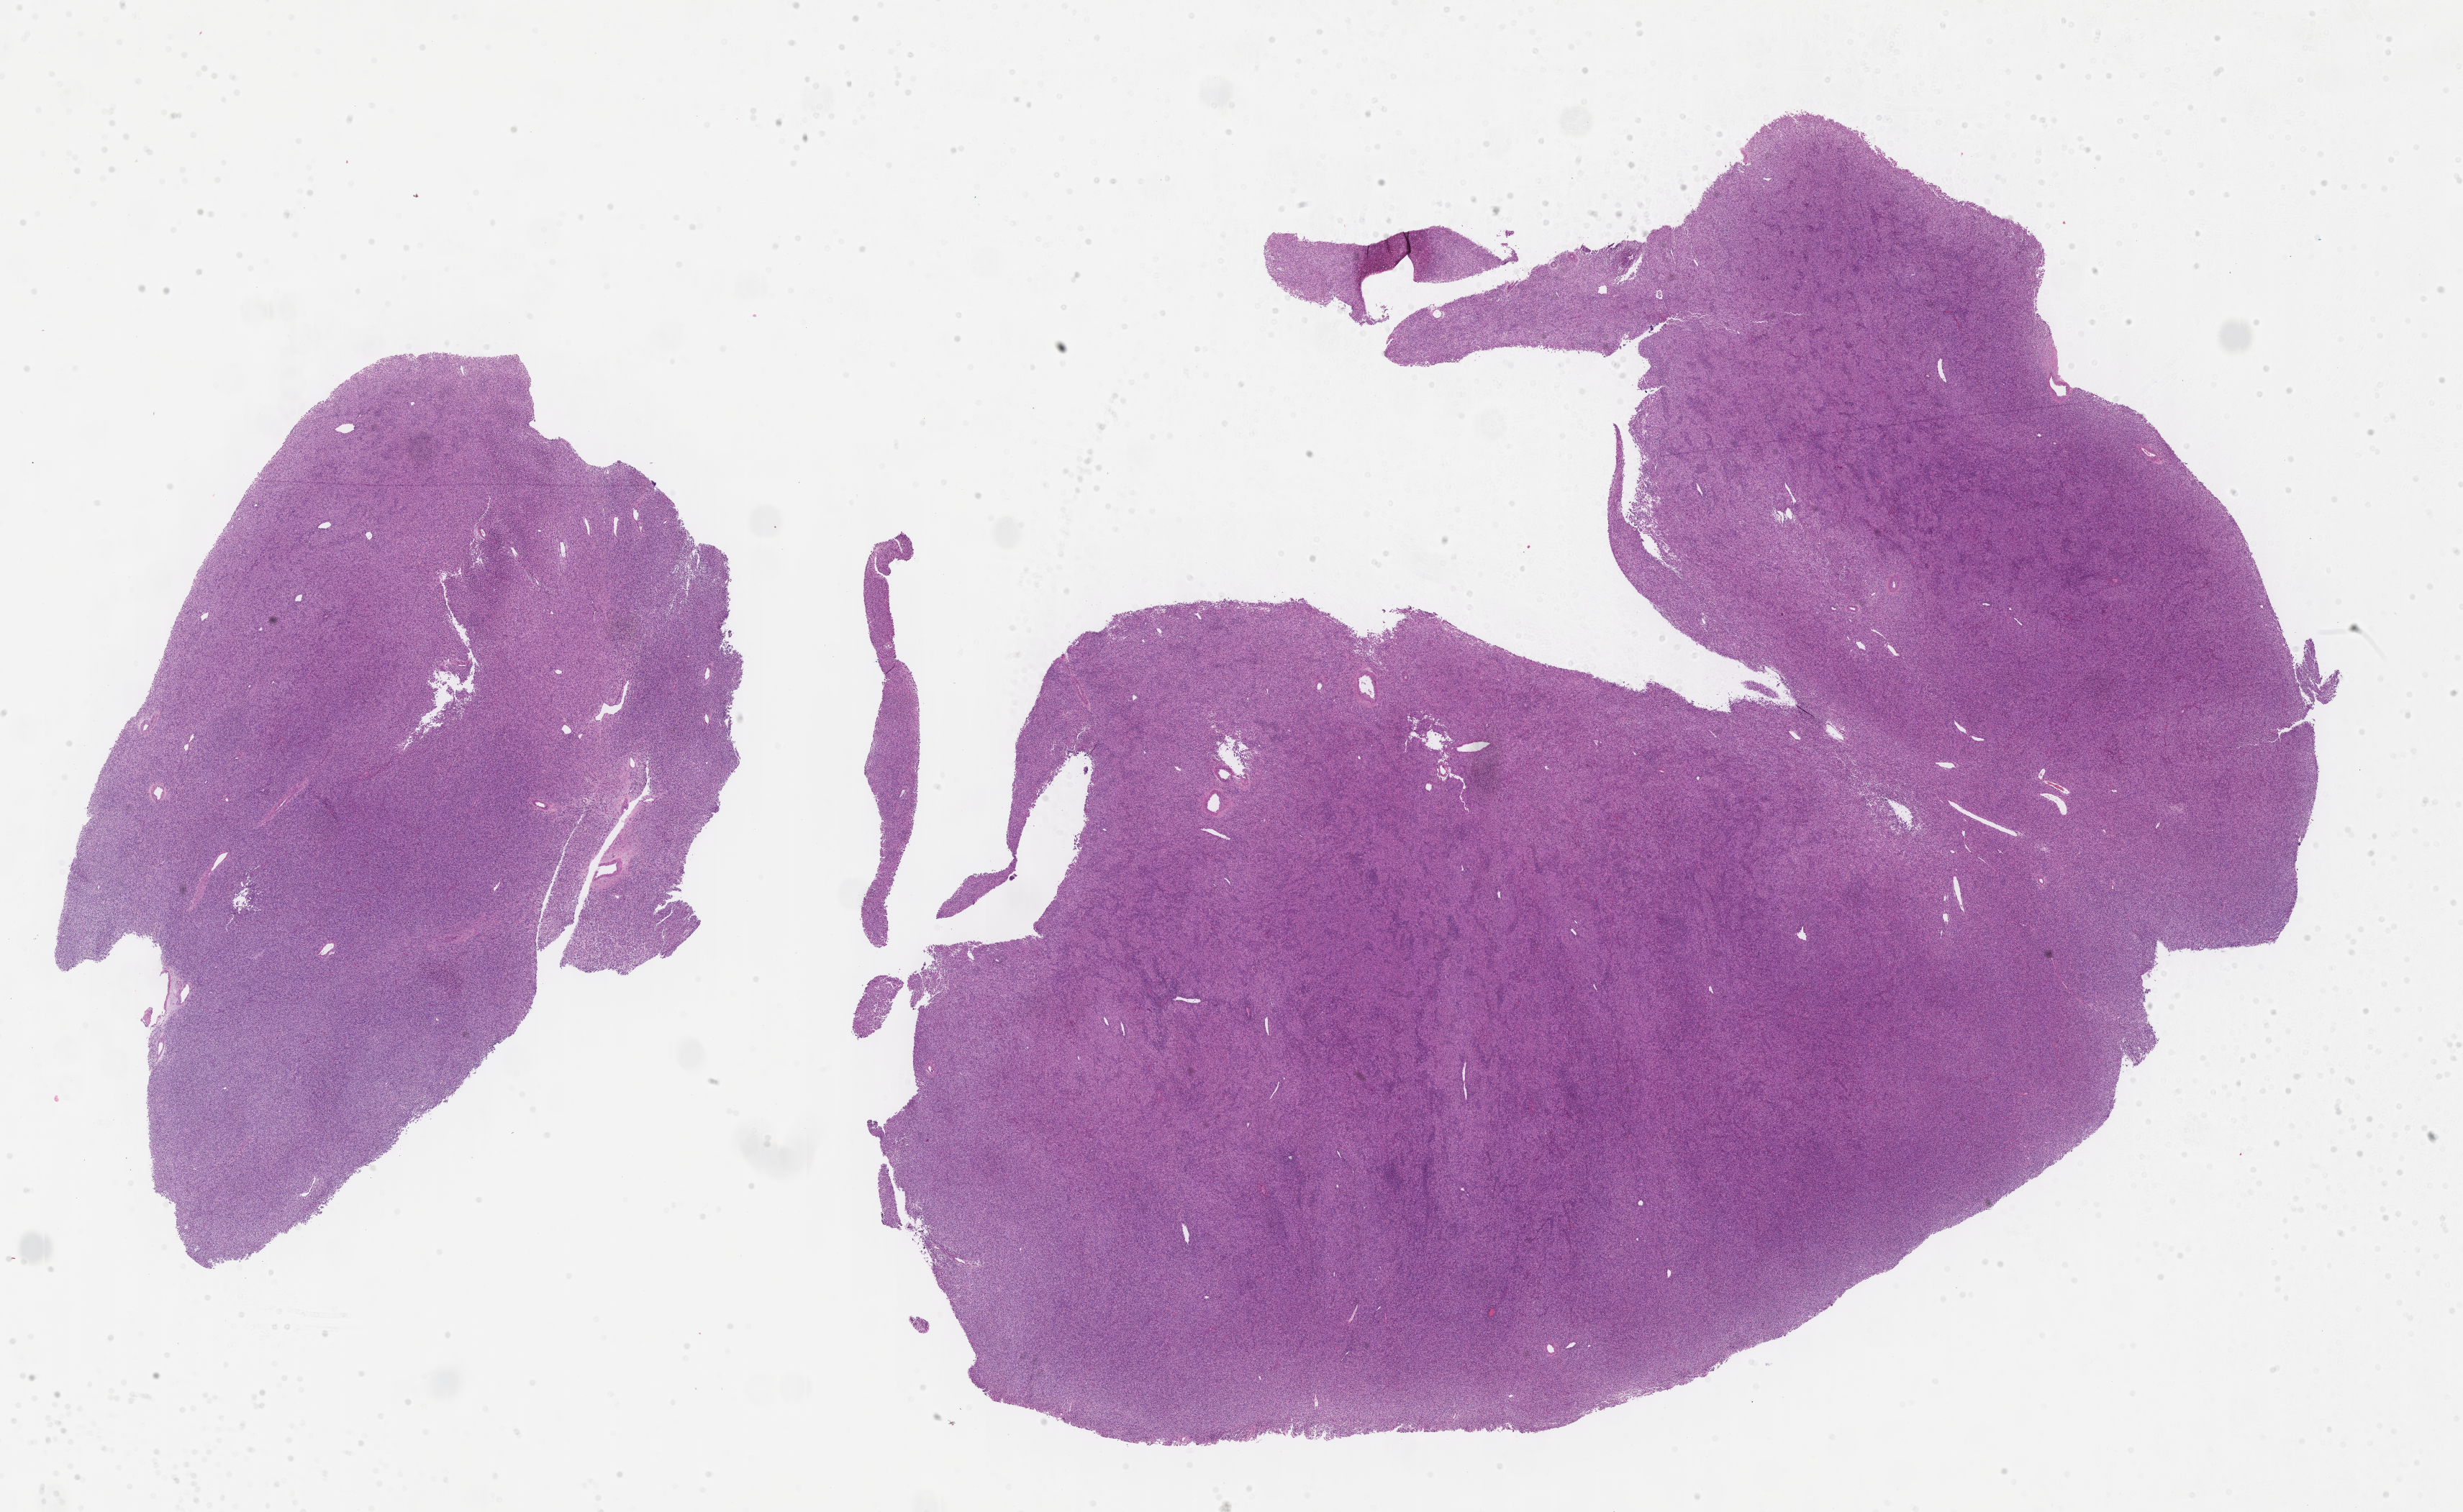
Digitized hematoxylin and eosin (H&E)-stained section of tumor tissue, low-resolution overview of the scanned area, about 27.7 x 17.0 mm, formalin-fixed, paraffin-embedded (FFPE) tissue, sample anatomic site: paratesticular, right. Patient: male, age 0.7 years at diagnosis.
- diagnosis: rhabdomyosarcoma; histological classification: spindle cell rhabdomyosarcoma
- stage (as recorded): 1